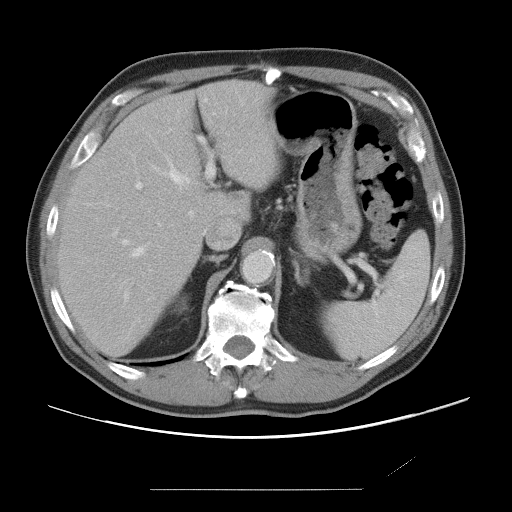
Contrast-enhanced abdominal CT, one axial slice; slice 49 of 87 in the series (ordered by position); 120 kVp; intravenous contrast given; soft-tissue window (W 400 / L 40 HU); 5 mm slice thickness; 512 × 512 image matrix, field of view 406 × 406 mm. Male patient, age 74 years. From the clinical record (not read from this slice): diagnosis: colorectal cancer liver metastases, imaged before liver resection; multiple liver metastases: yes; largest metastasis: 1.1 cm; disease in both lobes: no.
Outlined on this slice (outlined manually by an expert reader):
- hepatic veins: bounding box [x1, y1, x2, y2] px = [123, 113, 215, 256]
- liver: [59, 81, 279, 356]
- planned liver remnant (the part of the liver to remain after resection): [59, 81, 279, 356]
- portal vein (with intrahepatic branches): [113, 137, 215, 299]
- liver metastasis: [230, 196, 242, 203]